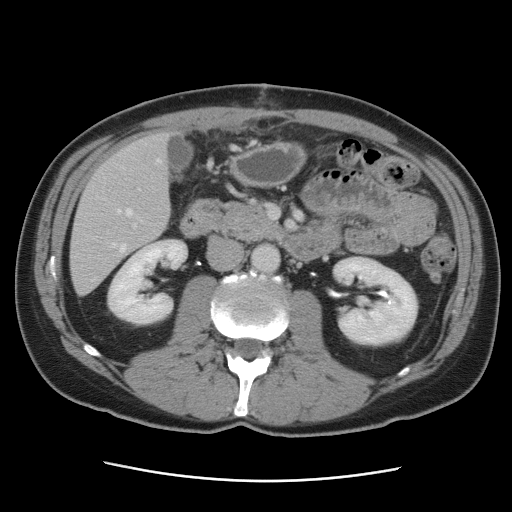
Contrast-enhanced abdominal CT, one axial slice. Position 33 of 89 along the scan axis. 120 kVp. Intravenous contrast given. Soft-tissue window (W 400 / L 40 HU). 5 mm slice thickness. 512 × 512 image matrix. Male patient, age 59 years. Case-level facts recorded for this patient, not image findings: diagnosis: colorectal cancer liver metastases, imaged before liver resection.
Structures marked on this image (outlined manually by an expert reader):
- hepatic veins: bounding box (x1, y1, x2, y2) in pixels: (94, 159, 161, 280)
- liver: (71, 133, 170, 294)
- planned liver remnant (the part of the liver to remain after resection): (74, 133, 170, 245)
- portal vein (with intrahepatic branches): (133, 189, 140, 228)